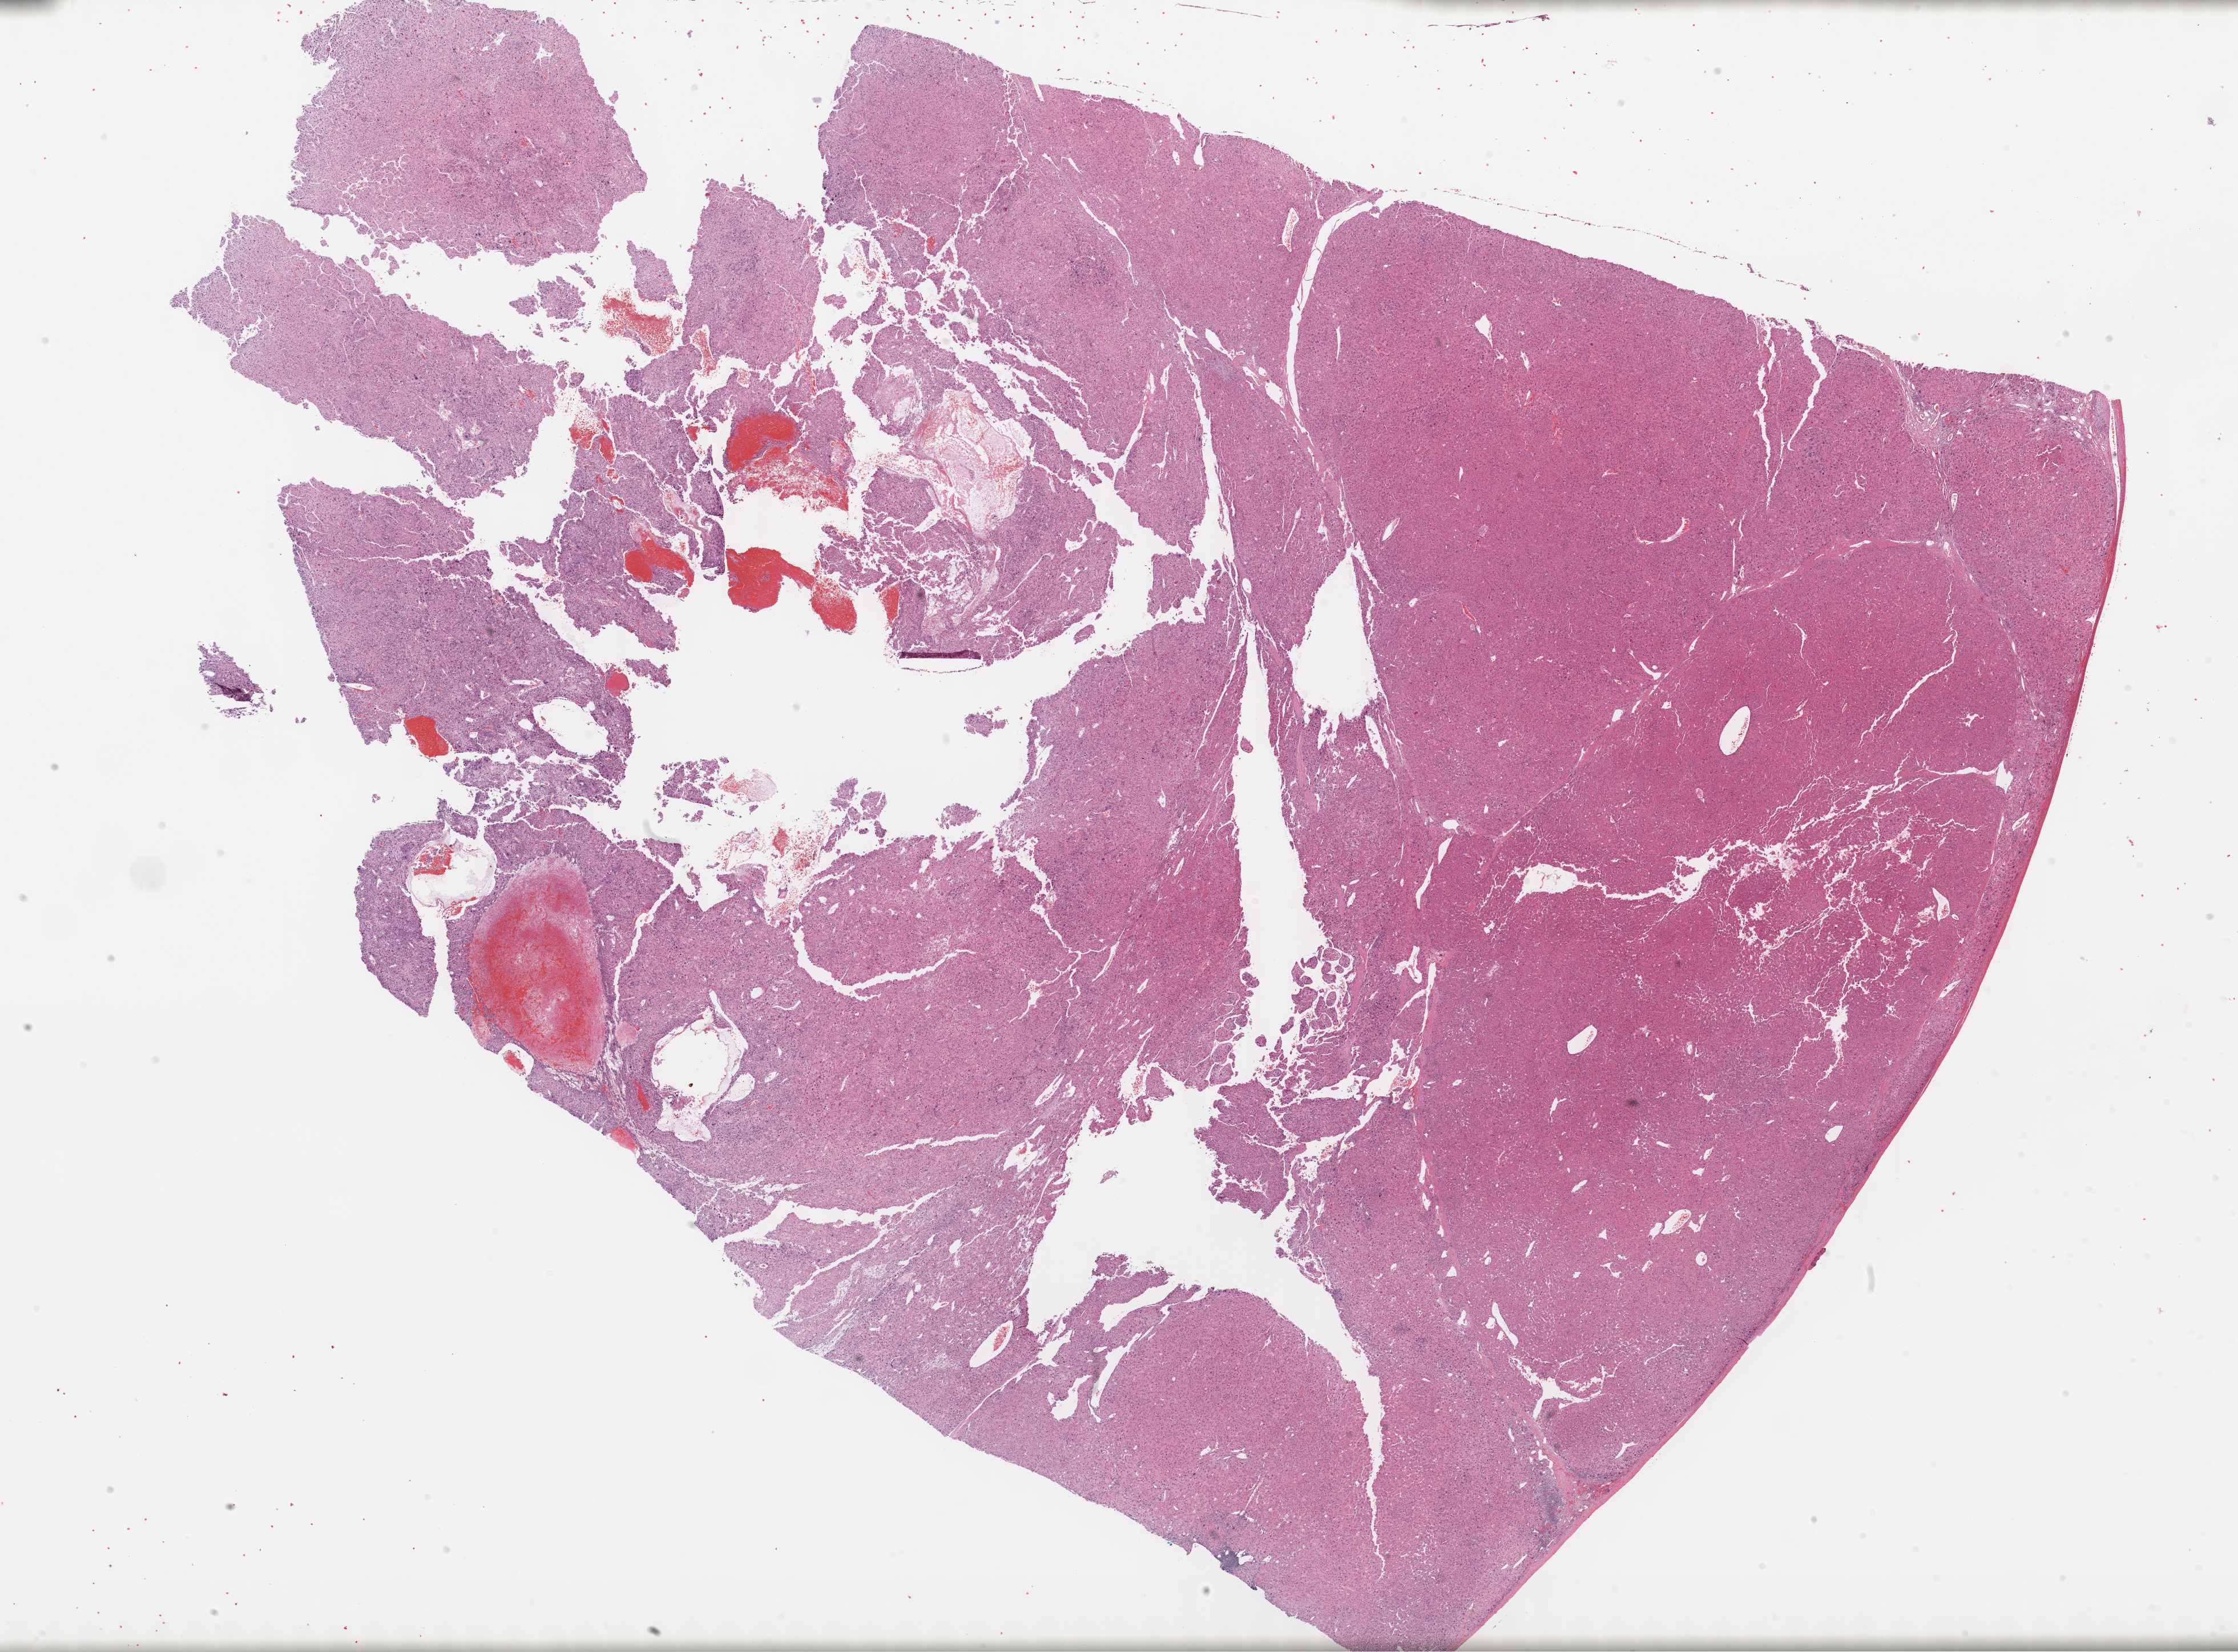
Digitized H&E tissue section (whole slide), a low-resolution overview of the entire scanned area, about 31.7 x 23.4 mm (acquisition: 40x scan); formalin-fixed paraffin-embedded (FFPE) diagnostic section; primary tumour sample from the liver. Patient: male, age at initial diagnosis 74 years. Histologic grade: G3 (poorly differentiated).
• AJCC pathologic stage: I
• pathologic diagnosis: Hepatocellular carcinoma, NOS